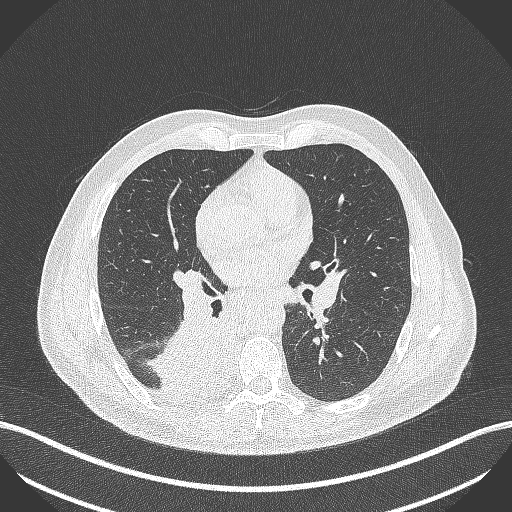
Chest CT, one axial slice; reconstruction kernel B70f; 100 kVp; lung window (W 1500 / L -600 HU); 512 × 512 image matrix. Patient: male, 61 years. From the clinical record (not read from this slice): clinical TNM (as recorded): T1 N0 M0; histopathological grade: G3.
Outlined on this slice (bounding box drawn by a radiologist):
- lung tumour (recorded histology: small cell carcinoma): bounding box <148,306,237,402> (left, top, right, bottom; pixels)